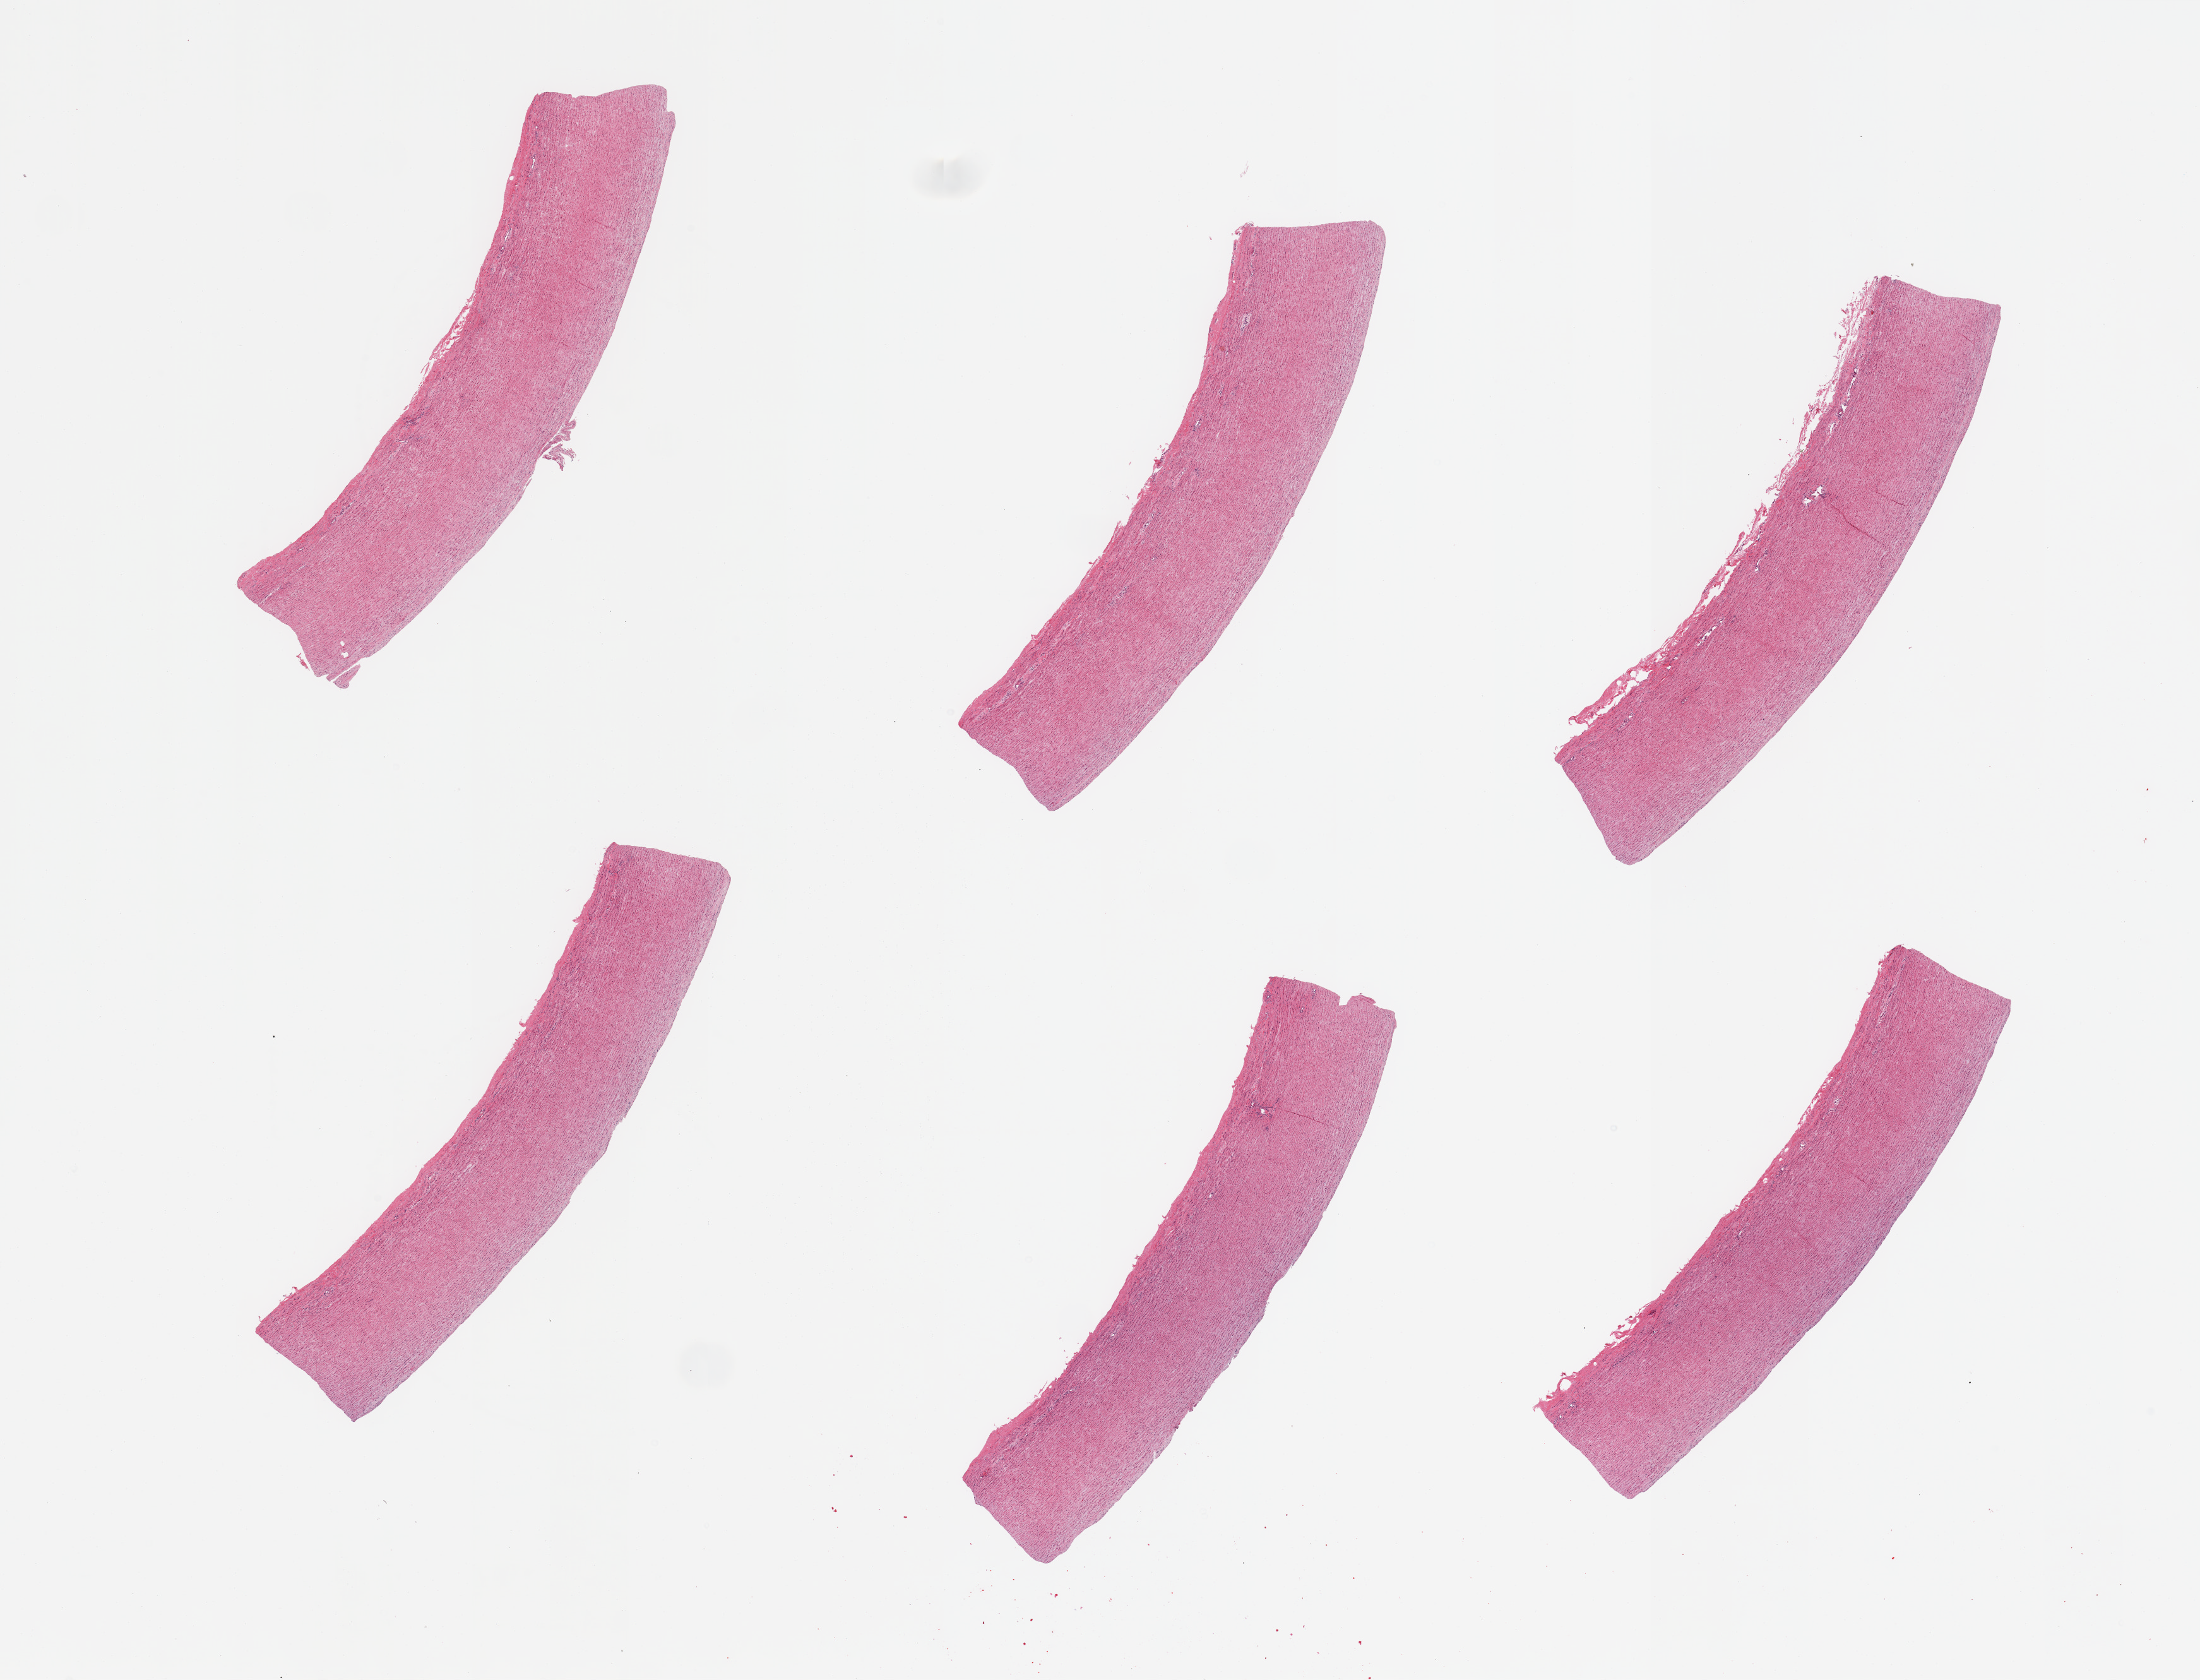
Digitized H&E-stained section — a low-resolution overview of the entire scanned area, about 27.6 x 21.0 mm. PAXgene-fixed, paraffin-embedded tissue. Section of aorta (target tissue). Tissue donor sample. Donor: male.
• reviewer comment on this tissue sample: 6 pieces; no plaques; well trimmed